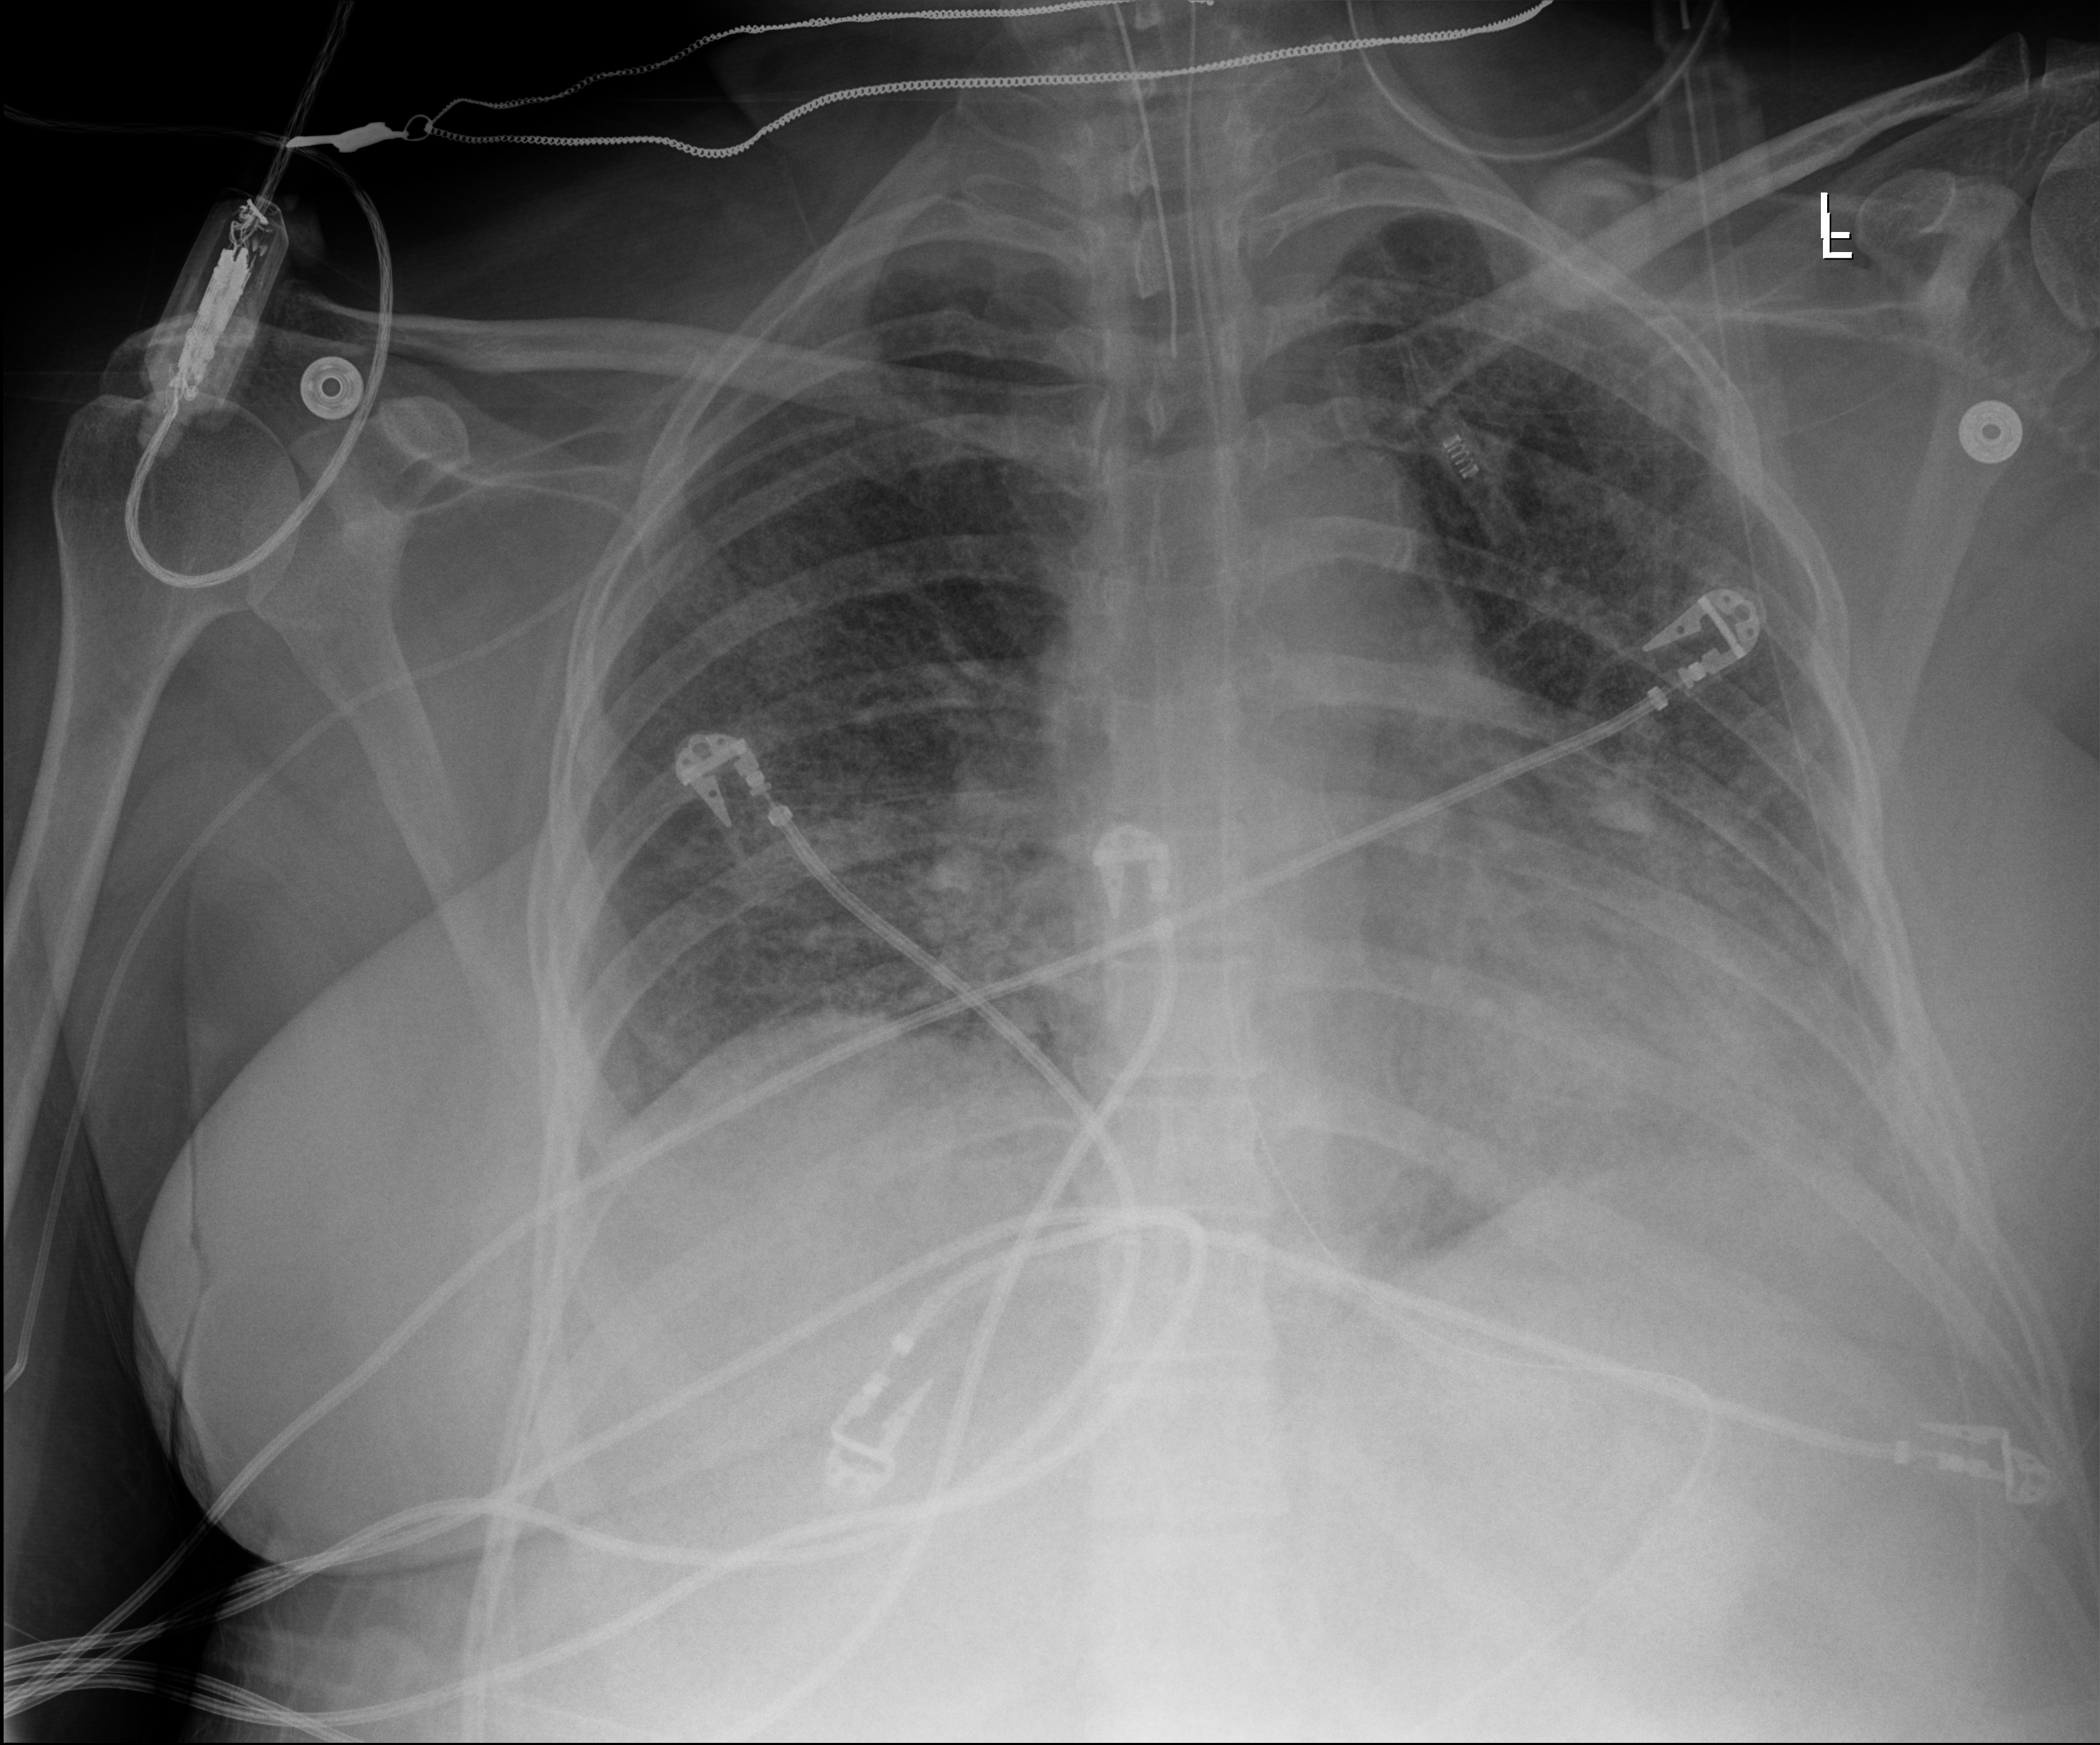
Chest X-ray (portable), anteroposterior (AP) projection. Female patient hospitalised with COVID-19, age 18–59 years.
Admission-level facts for this patient (not findings on this image; timing relative to this image not recorded): admitted to intensive care during this hospital stay: yes; mechanically ventilated during this hospital stay: yes.